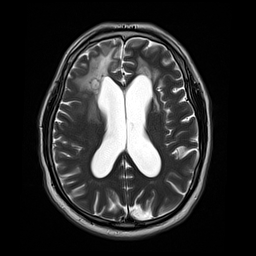
Brain MRI from a brain-tumour surgery series, one axial slice. Position 19 of 44 along the scan axis. 4 mm slice thickness. 256 × 256 image matrix, field of view 240 × 240 mm. Case-level facts recorded for this patient, not image findings: histopathology: Astrocytoma; WHO grade: 4; IDH mutation: yes; tumour location: Right Frontal.
Annotated regions visible in this slice (outlined manually by an expert reader):
- tumour: bounding box <90,106,98,119> (left, top, right, bottom; pixels)